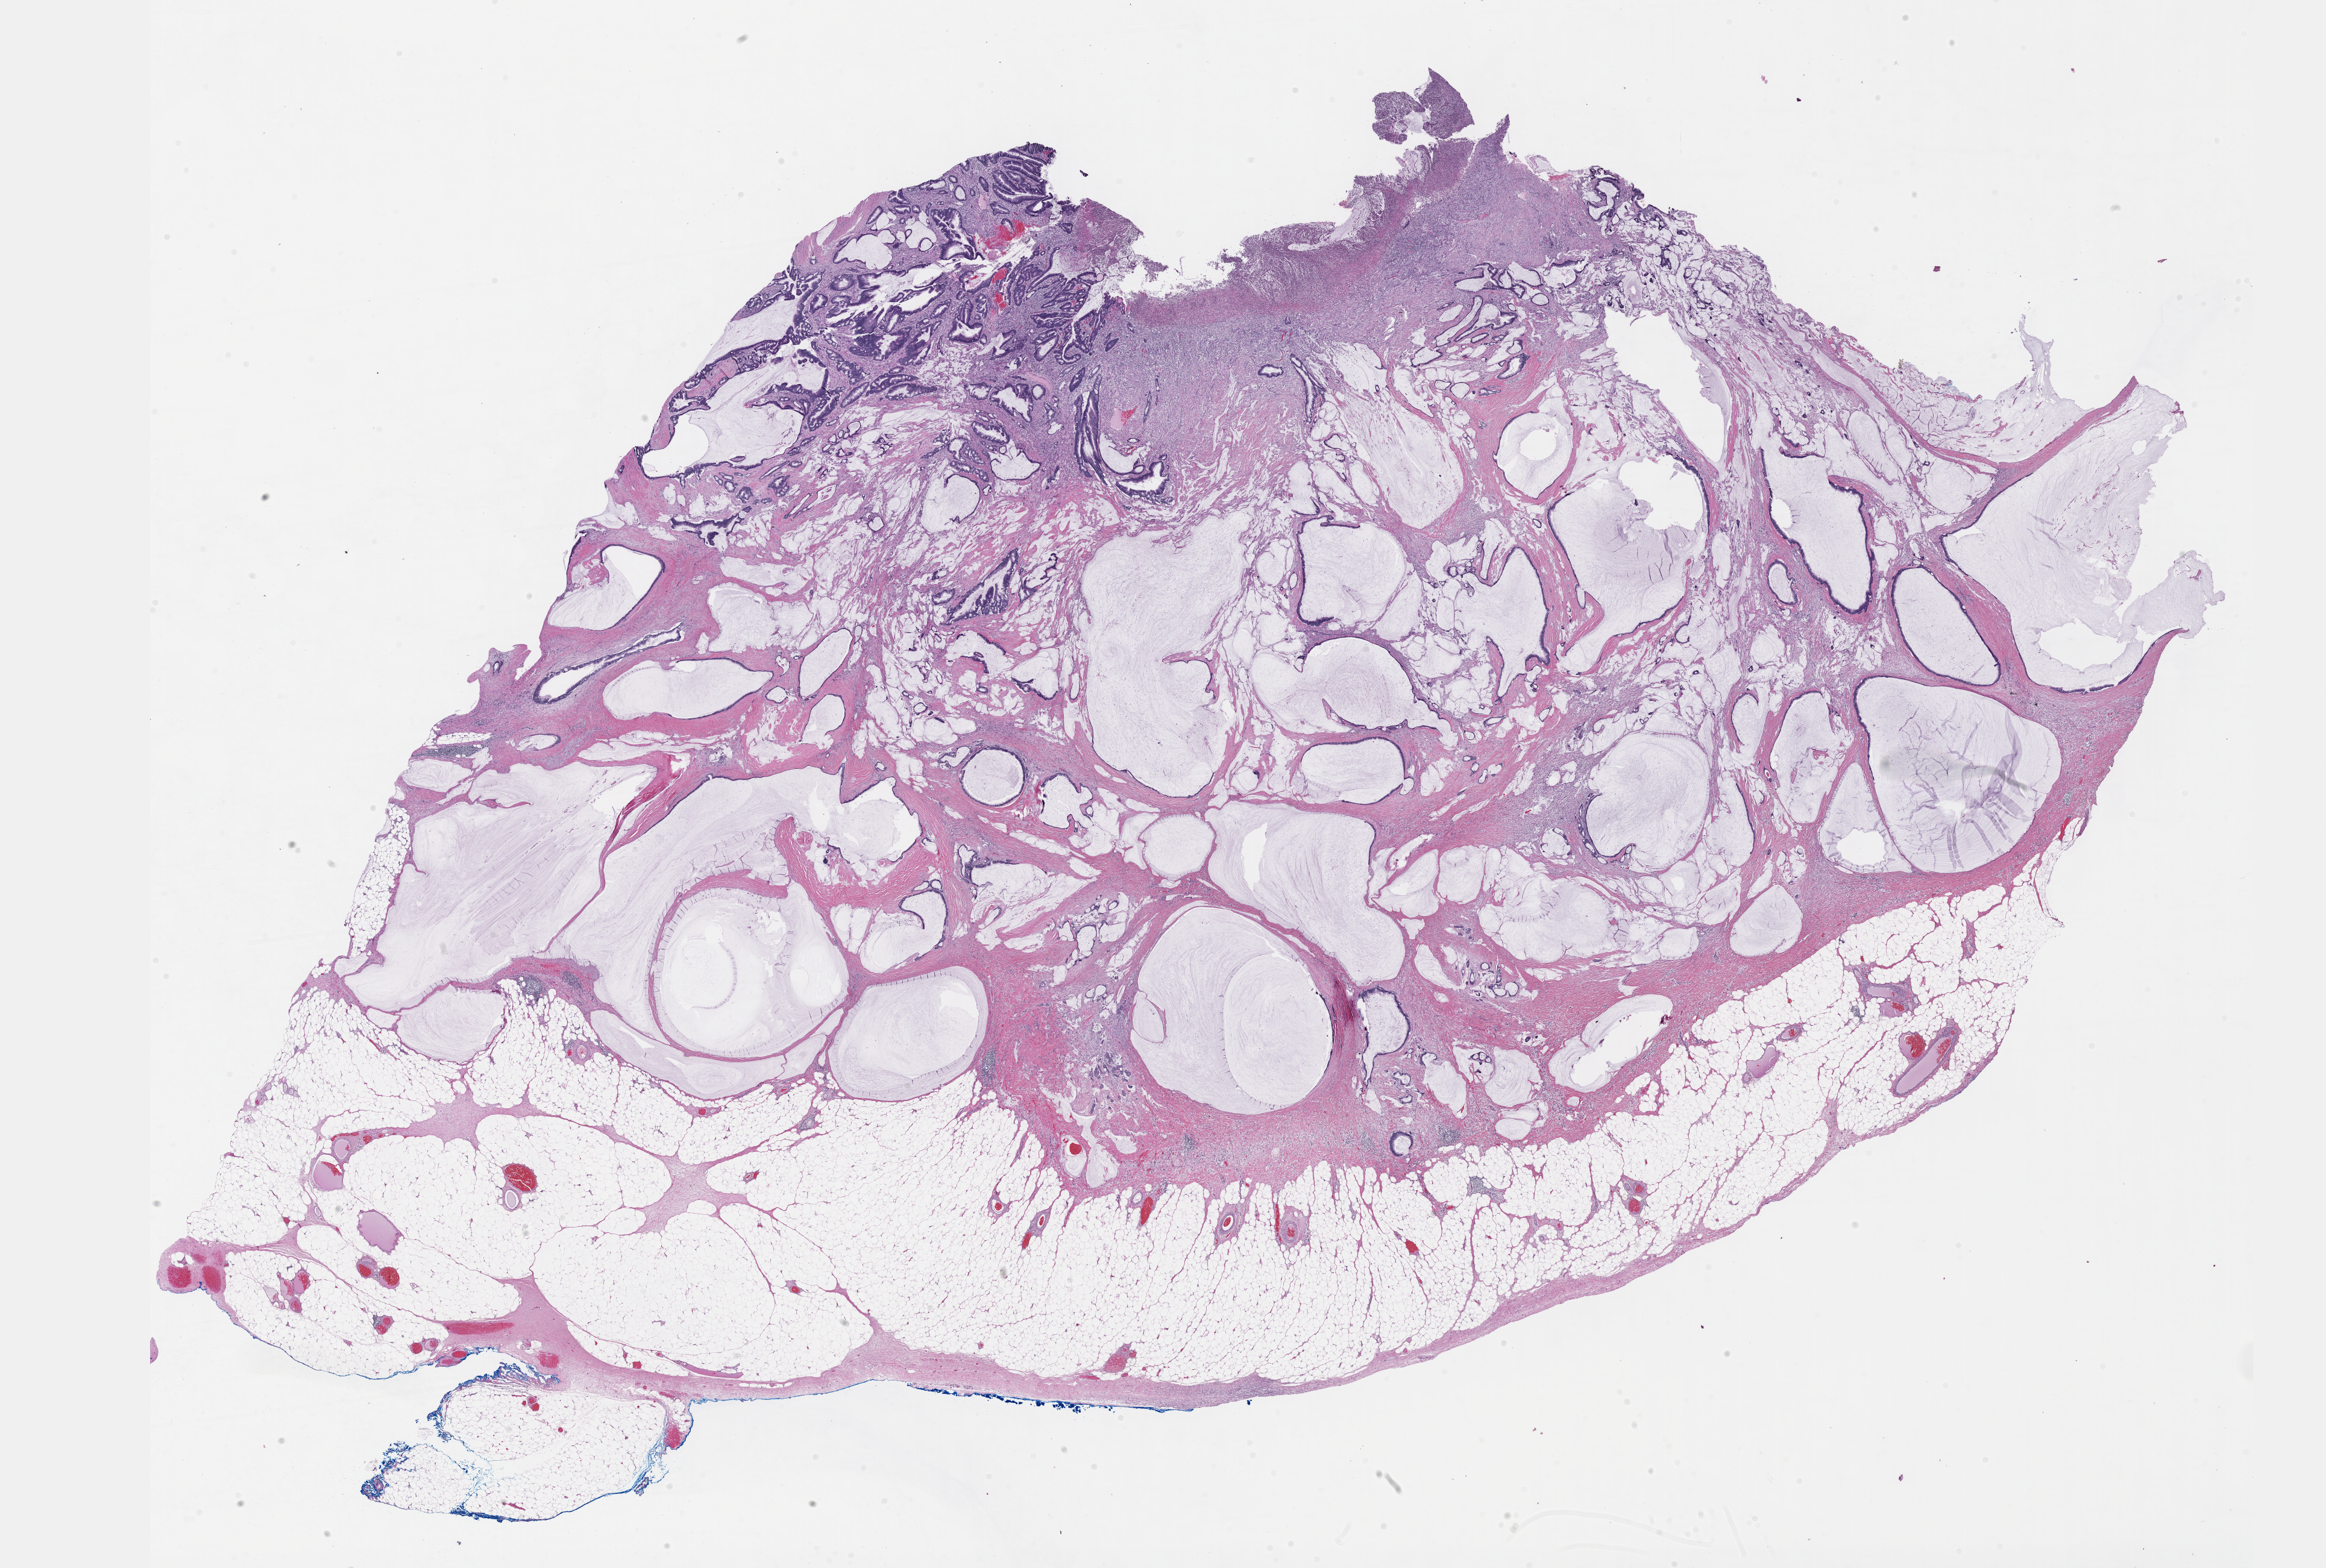
Digitized H&E tissue section (whole slide) — a low-resolution overview of the entire scanned area, about 31.2 x 21.0 mm; formalin-fixed paraffin-embedded (FFPE) diagnostic section; metastatic tumour sample, sampled site not recorded. Patient: female, age at initial diagnosis 66 years.
* this section: metastatic tumour tissue
* patient diagnosis: Mucinous adenocarcinoma (primary site: descending colon)